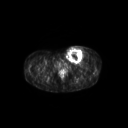
FDG PET of an extremity soft-tissue mass (from a PET/CT study), one axial slice; position 60 of 267 along the scan axis; 3.27 mm slice thickness; 128 × 128 image matrix, field of view 600 × 600 mm. Patient: female, 24 years. Case-level facts recorded for this patient, not image findings: histological type: leiomyosarcoma; grade: high; site of the primary tumour: groin.
Structures marked on this image (expert contour drawn on MRI and transferred to this co-registered scan by the dataset authors):
- gross tumour volume including surrounding oedema: bounding box <64,45,89,64> (left, top, right, bottom; pixels)
- gross tumour volume (mass): <64,46,84,63>